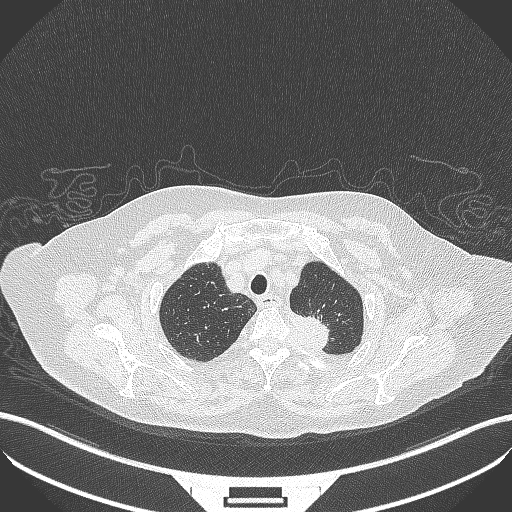
Chest CT, one axial slice; slice 296 of 353 in the series (ordered by position); reconstruction kernel B70f; 100 kVp; lung window (W 1500 / L -600 HU); 1 mm slice thickness; 512 × 512 image matrix, field of view 400 × 400 mm. Female patient, age 81 years. Case-level facts recorded for this patient, not image findings: clinical TNM (as recorded): T2a N0 M0.
Structures marked on this image (rectangle marked by the reading radiologist):
- lung tumour (recorded histology: adenocarcinoma): bounding box <287,308,331,355> (left, top, right, bottom; pixels)